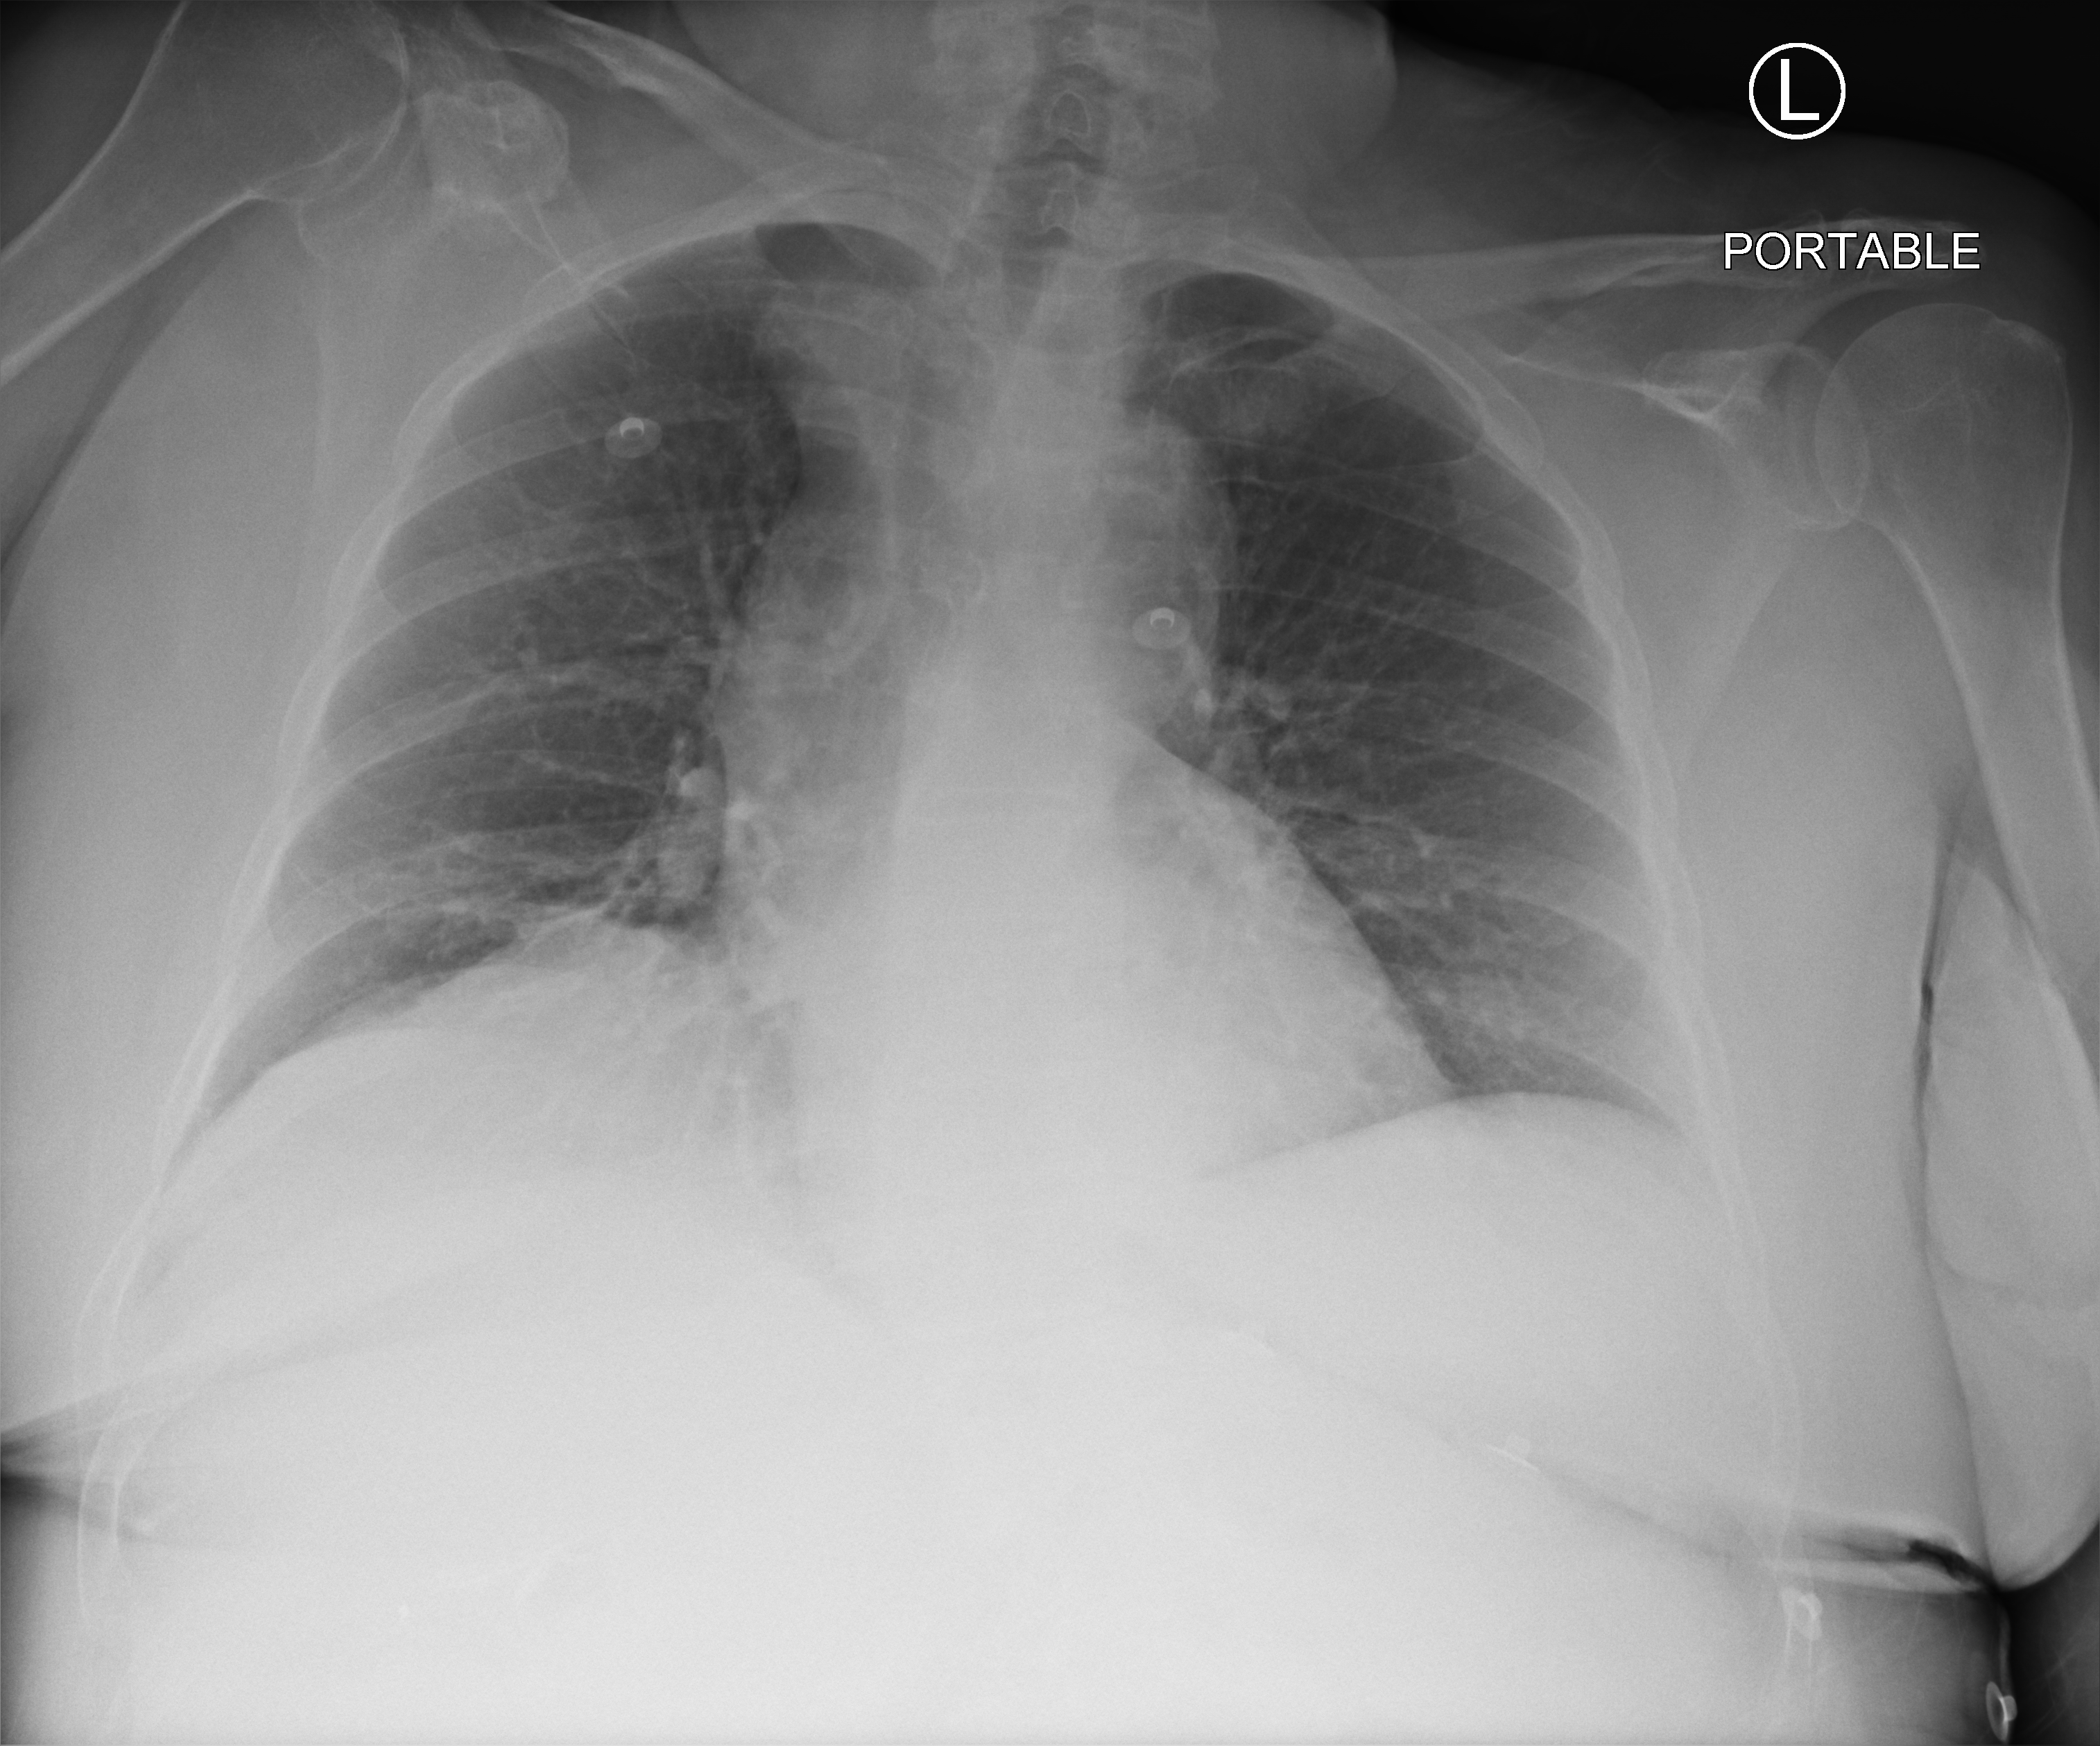
Bedside chest radiograph (computed radiography), anteroposterior (AP) projection. Female patient hospitalised with COVID-19, age 75–90 years.
From the hospital-stay record, not from the radiograph (when in the stay this image was taken is not recorded): other chronic lung disease (admission record): no; admitted to intensive care during this hospital stay: no.